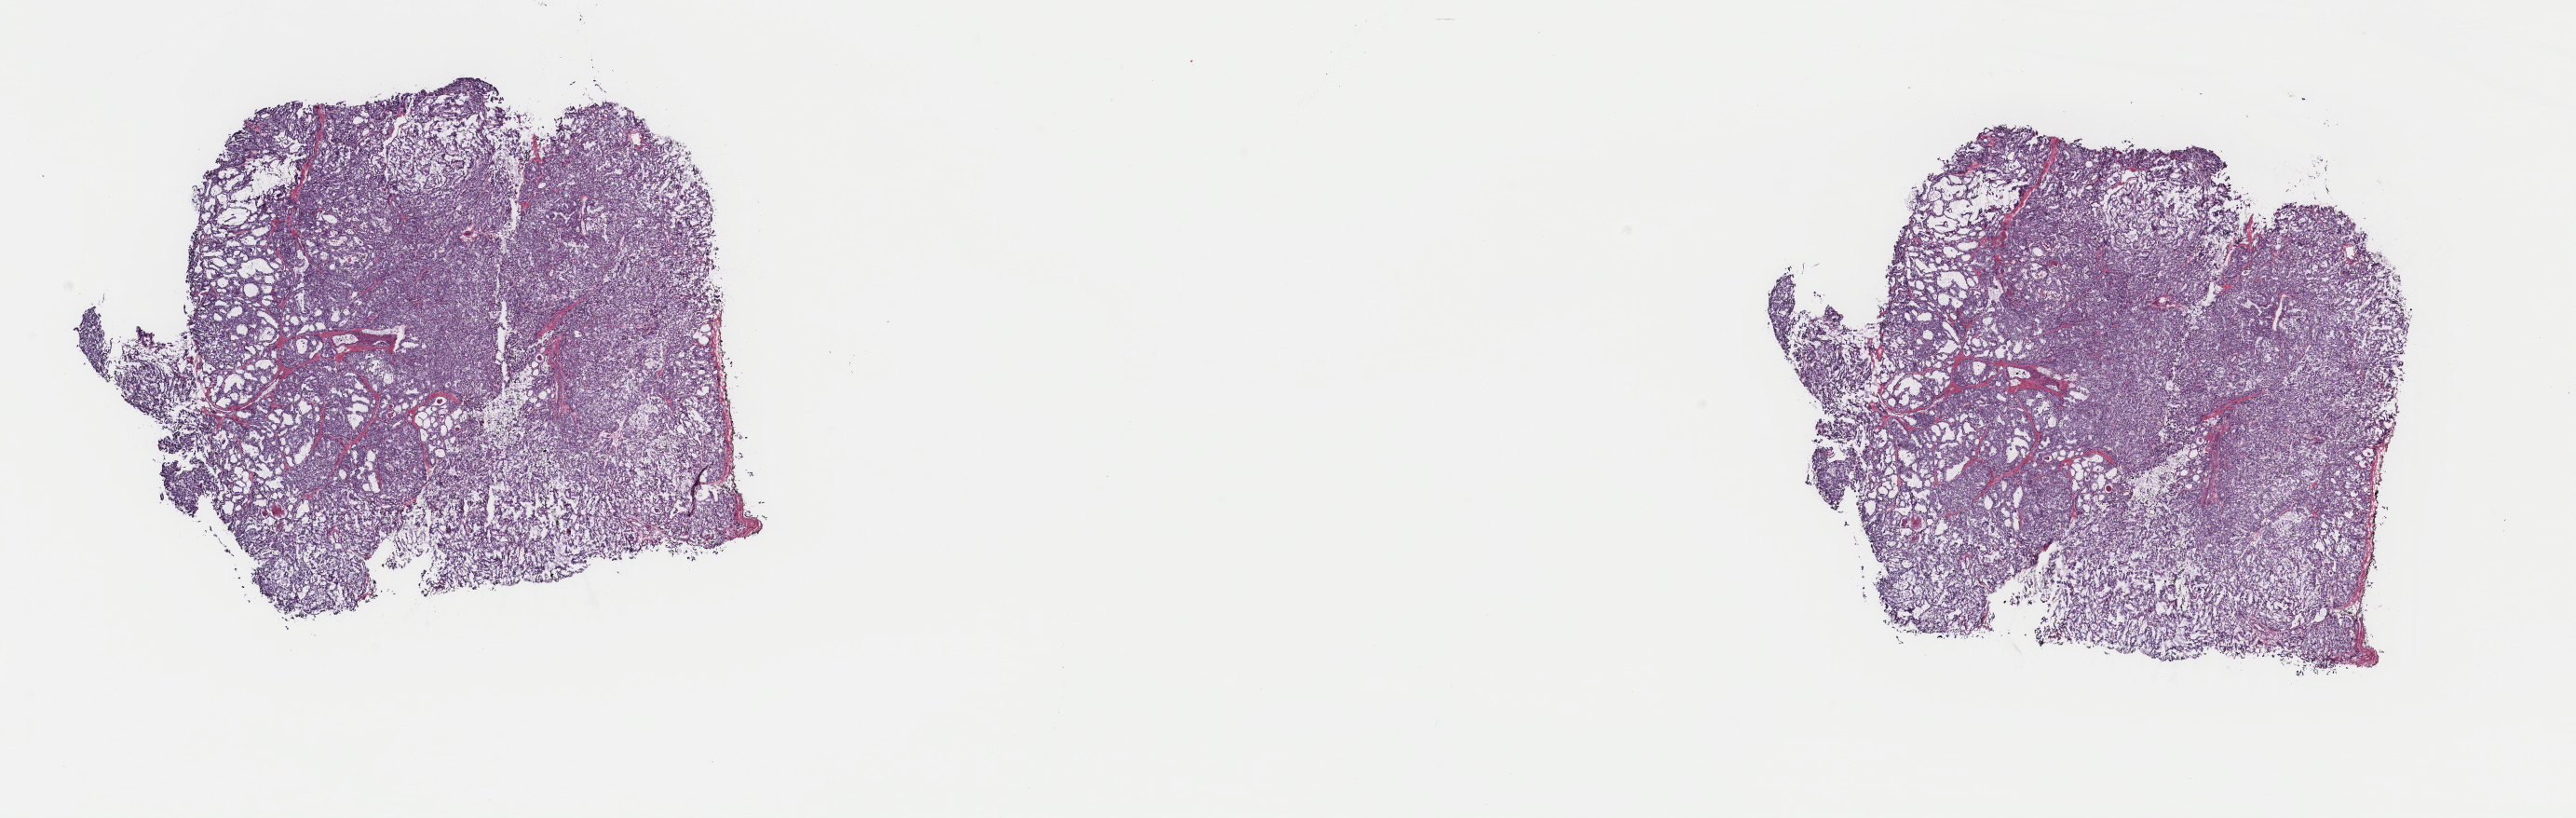
Whole-slide histology image, H&E, whole scanned area (about 22.0 x 7.0 mm, acquisition: 40x scan) shown as a low-resolution overview; frozen section; sample: primary tumour, thyroid. Female, age 41 years at initial diagnosis. Slide review estimates, as recorded: tumour cells 90%, tumour nuclei 100%, normal cells 0%, stromal cells 10%, necrosis 0%. Inflammatory infiltration, as recorded: lymphocyte infiltration 0%, monocyte infiltration 2%, neutrophil infiltration 0%.
Lymph nodes positive (case pathology): 0 of 3 examined. Laterality: left. AJCC pathologic stage: I (7th edition). Diagnosis: Papillary carcinoma, follicular variant (thyroid gland).